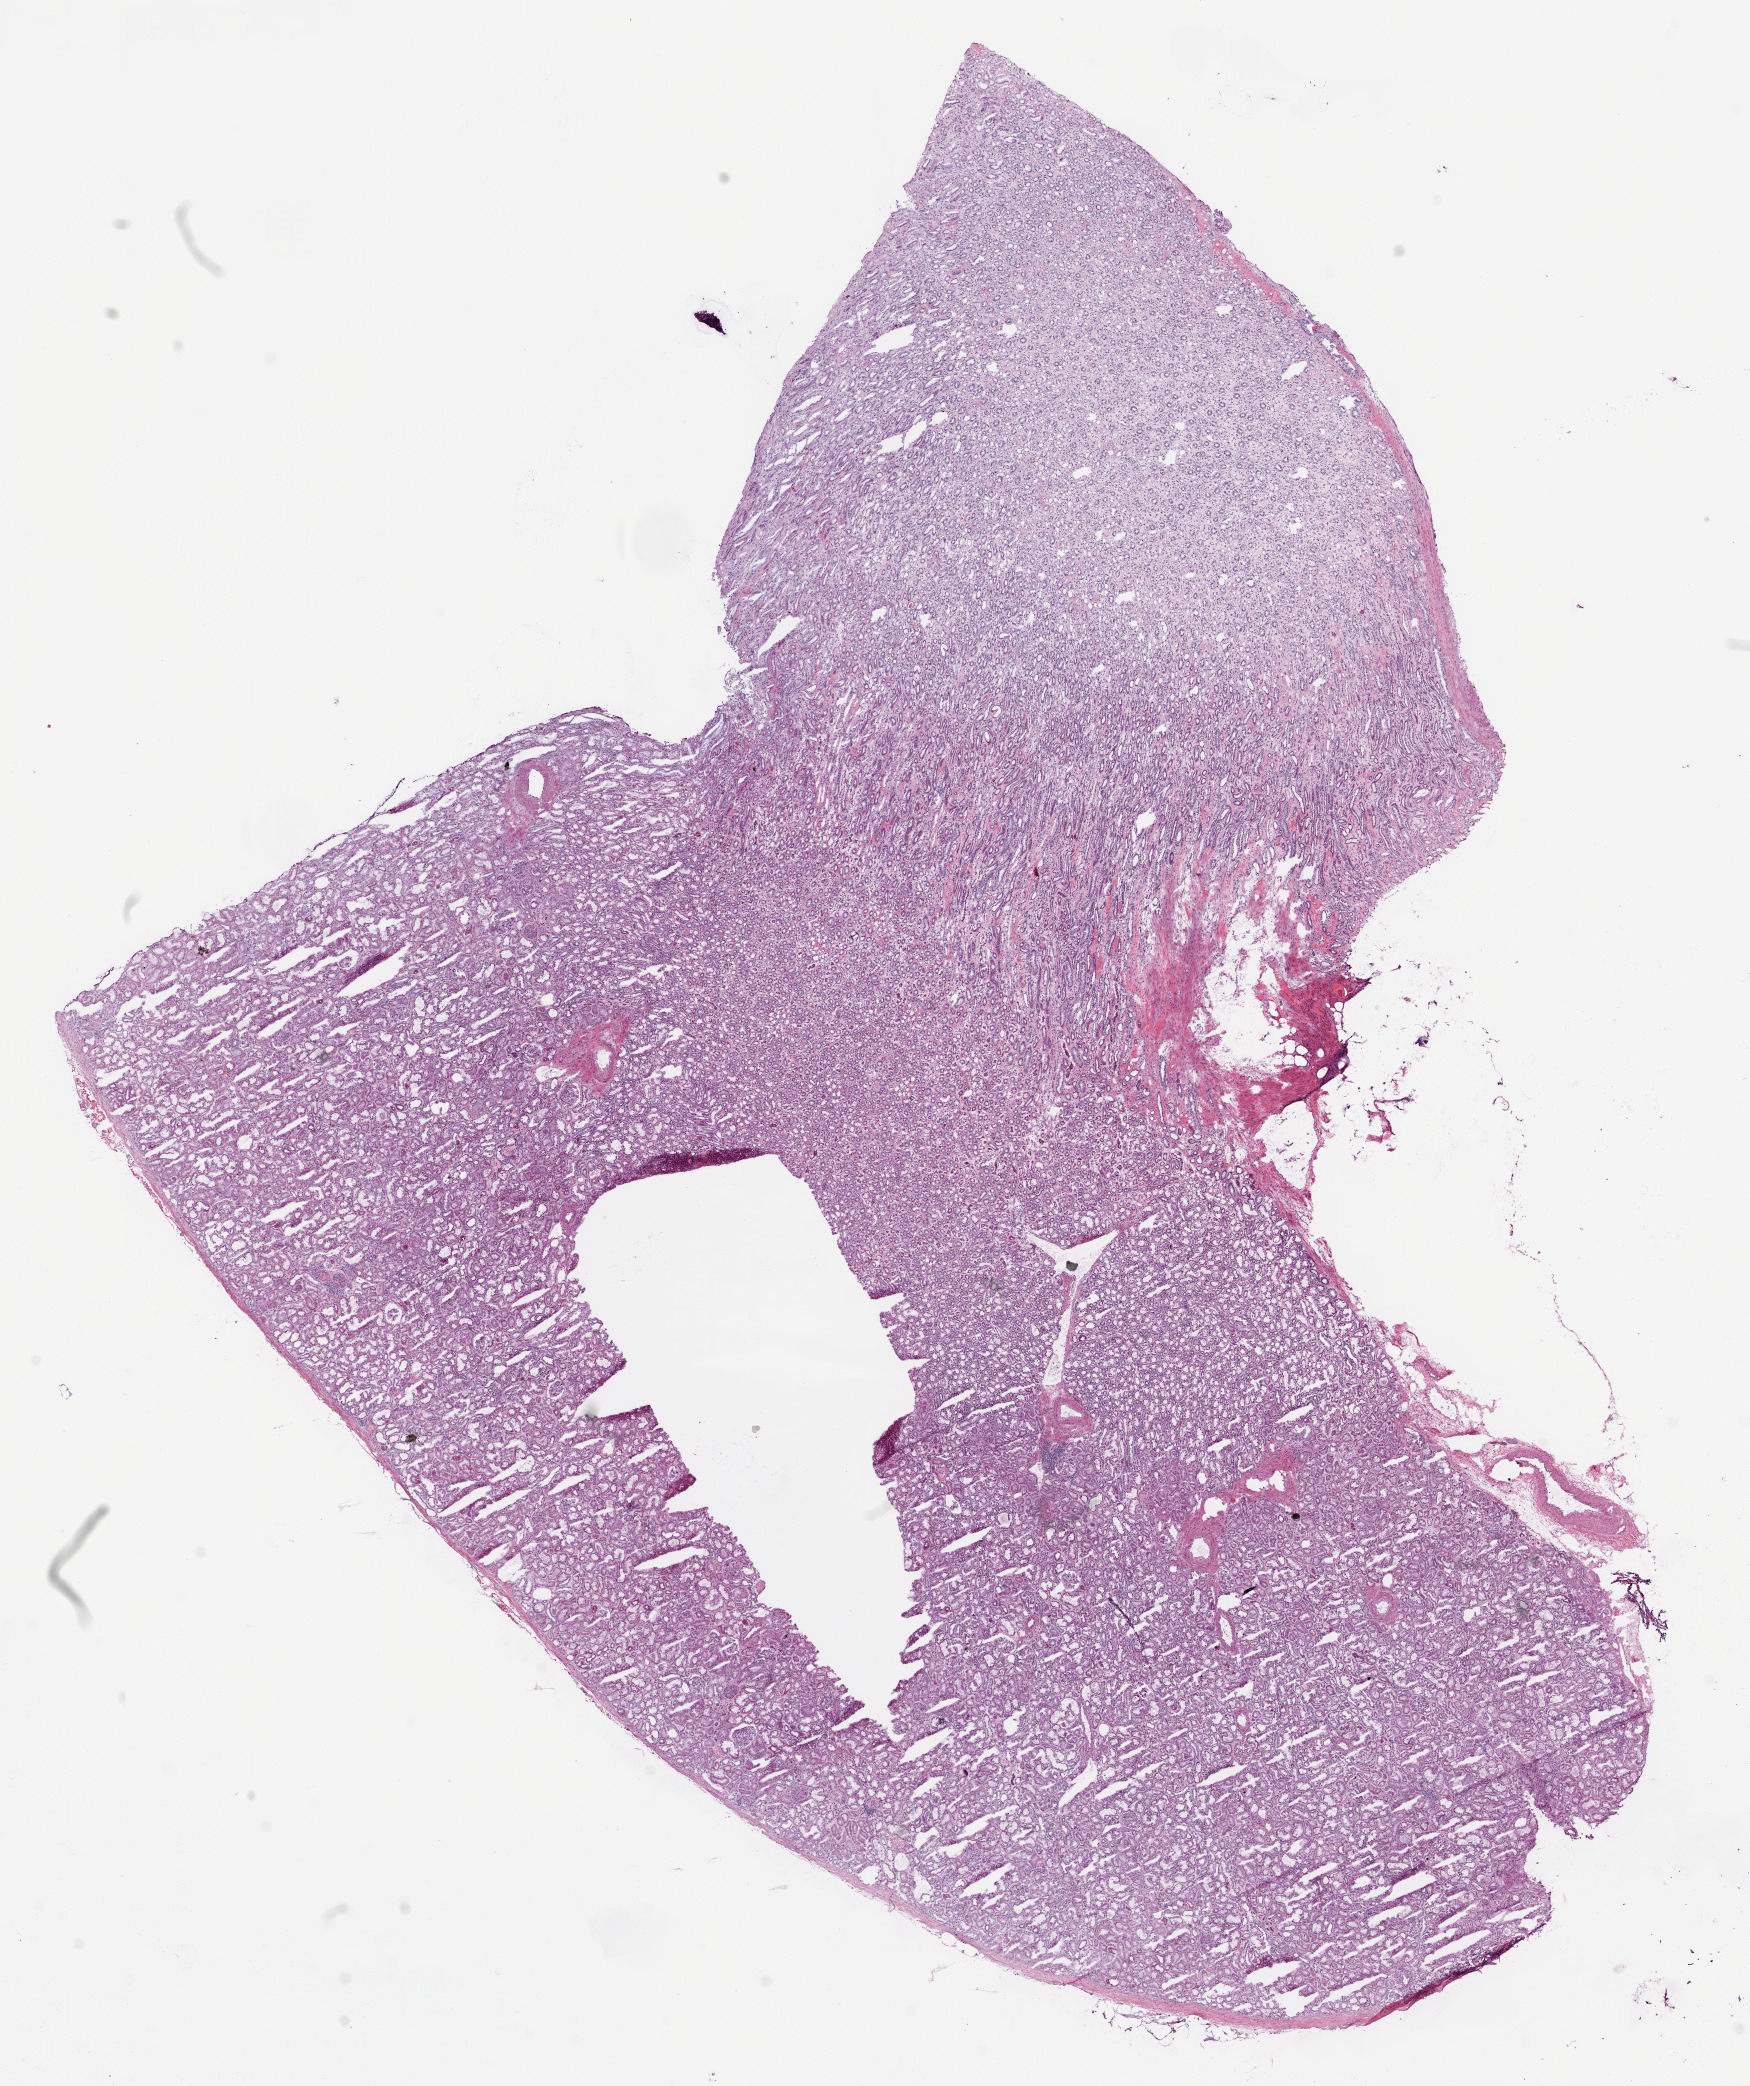
Digitized H&E-stained tissue section (whole slide), shown as a low-resolution overview of the whole scanned area (about 14.0 x 16.7 mm, from a 20x scan); frozen section from the bottom of the tissue portion; kidney, solid tissue normal (non-tumour tissue) sample. Female patient; age at initial diagnosis 64 years.
This section: solid tissue normal (non-tumour) sample from the same patient. Patient diagnosis: Clear cell adenocarcinoma, NOS.